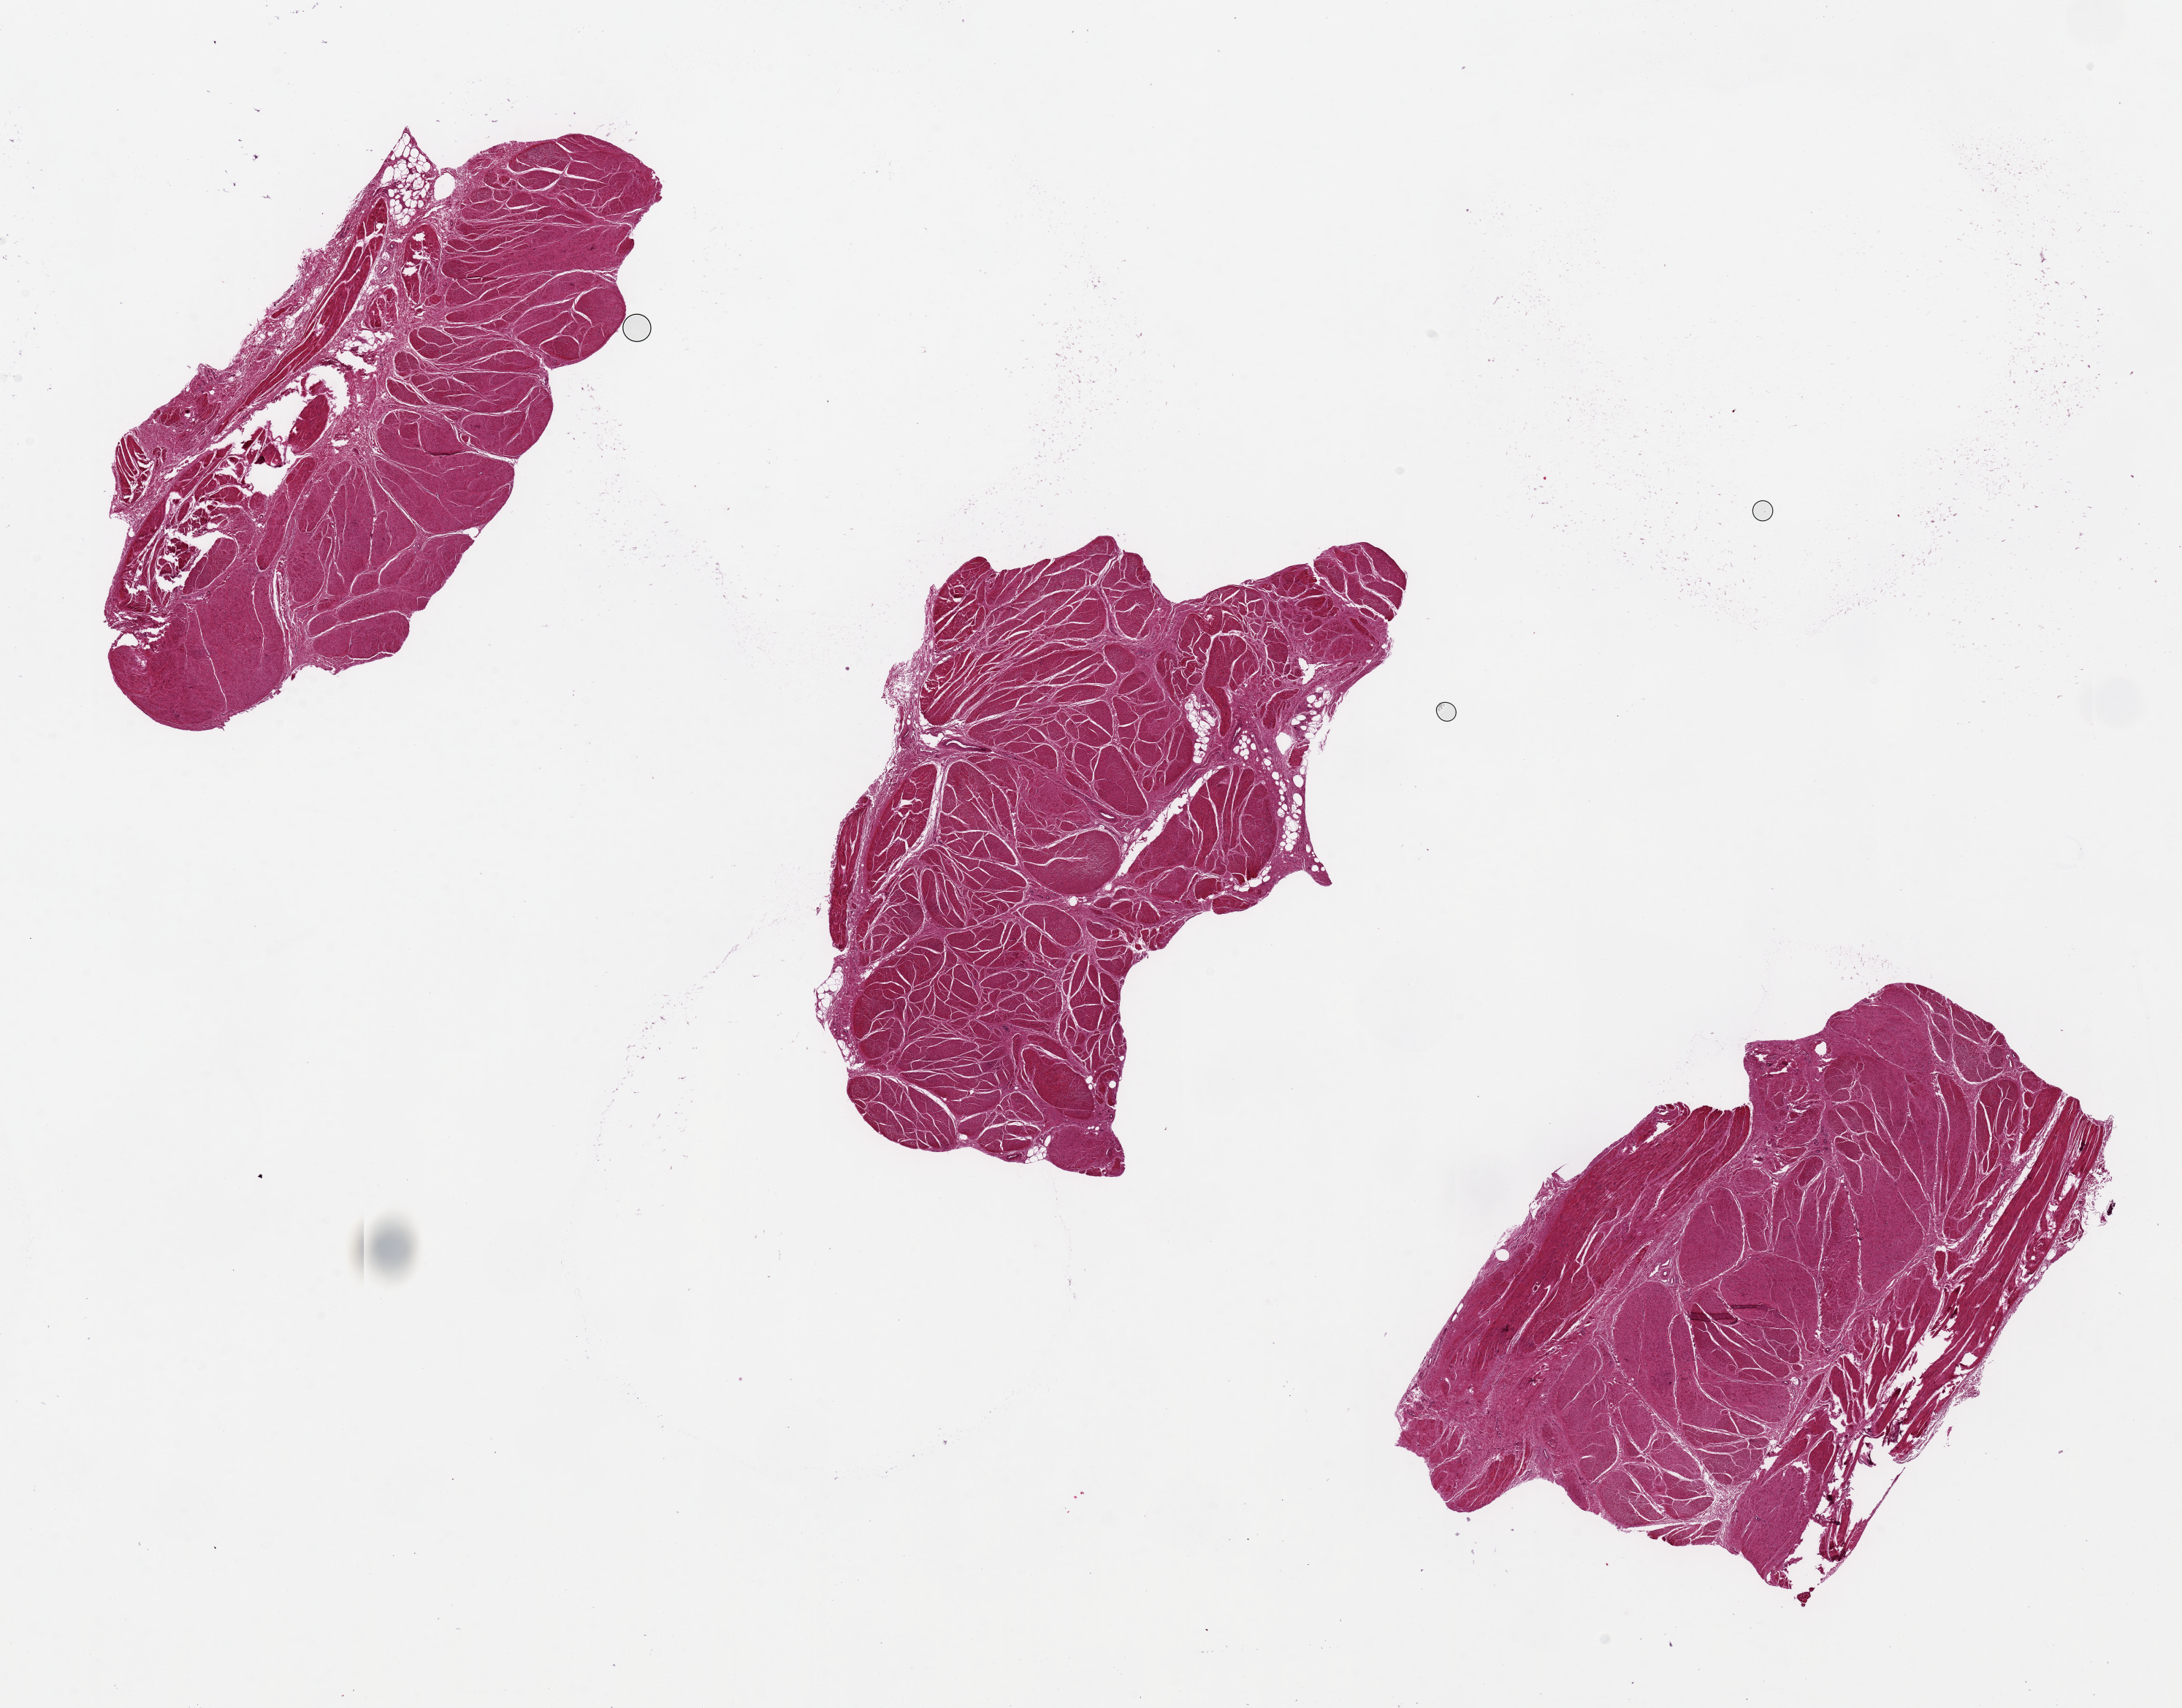
Digitized haematoxylin and eosin-stained section, brightfield — shown as a low-resolution overview of the whole scanned area (about 23.6 x 18.5 mm); PAXgene-fixed, paraffin-embedded tissue; section of urinary bladder (target tissue); tissue donor sample. Donor: male.
Pathologist's review note for this sample: 3 pieces. Mucosa missing/sloughed. Muscle intact.